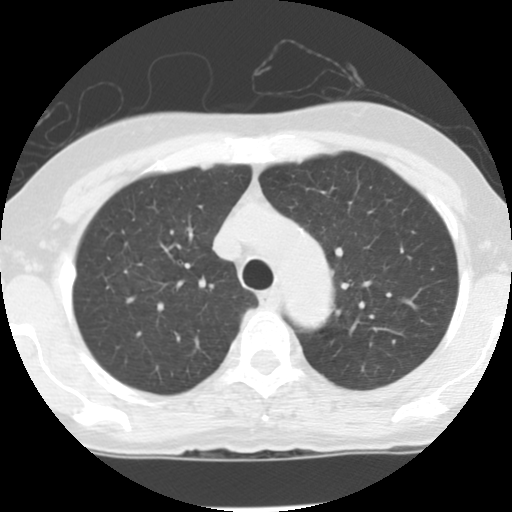
Chest CT (low-dose screening protocol), one axial image, baseline screening round, lung window (W 1500 / L -600 HU), 2.5 mm slice thickness, slice 28 of 134 in the series, 512 × 512 image matrix, field of view 290 × 290 mm. Female participant, aged 62 years at enrolment. Current smoker at enrolment.
Lesion marked by an expert reader, box from (x=100, y=249) to (x=148, y=293) px. The exam's reader record, not a measurement of the box and not confirmed to be the same lesion: non-calcified nodule or mass ≥4 mm, right upper lobe, 7 × 5 mm, poorly defined margins, ground glass attenuation. Lung cancer was diagnosed 875 days after this screen (after the third annual screen): bronchiolo-alveolar adenocarcinoma, NOS, right upper lobe, stage IA (AJCC 6th edition), 10 mm at pathology.